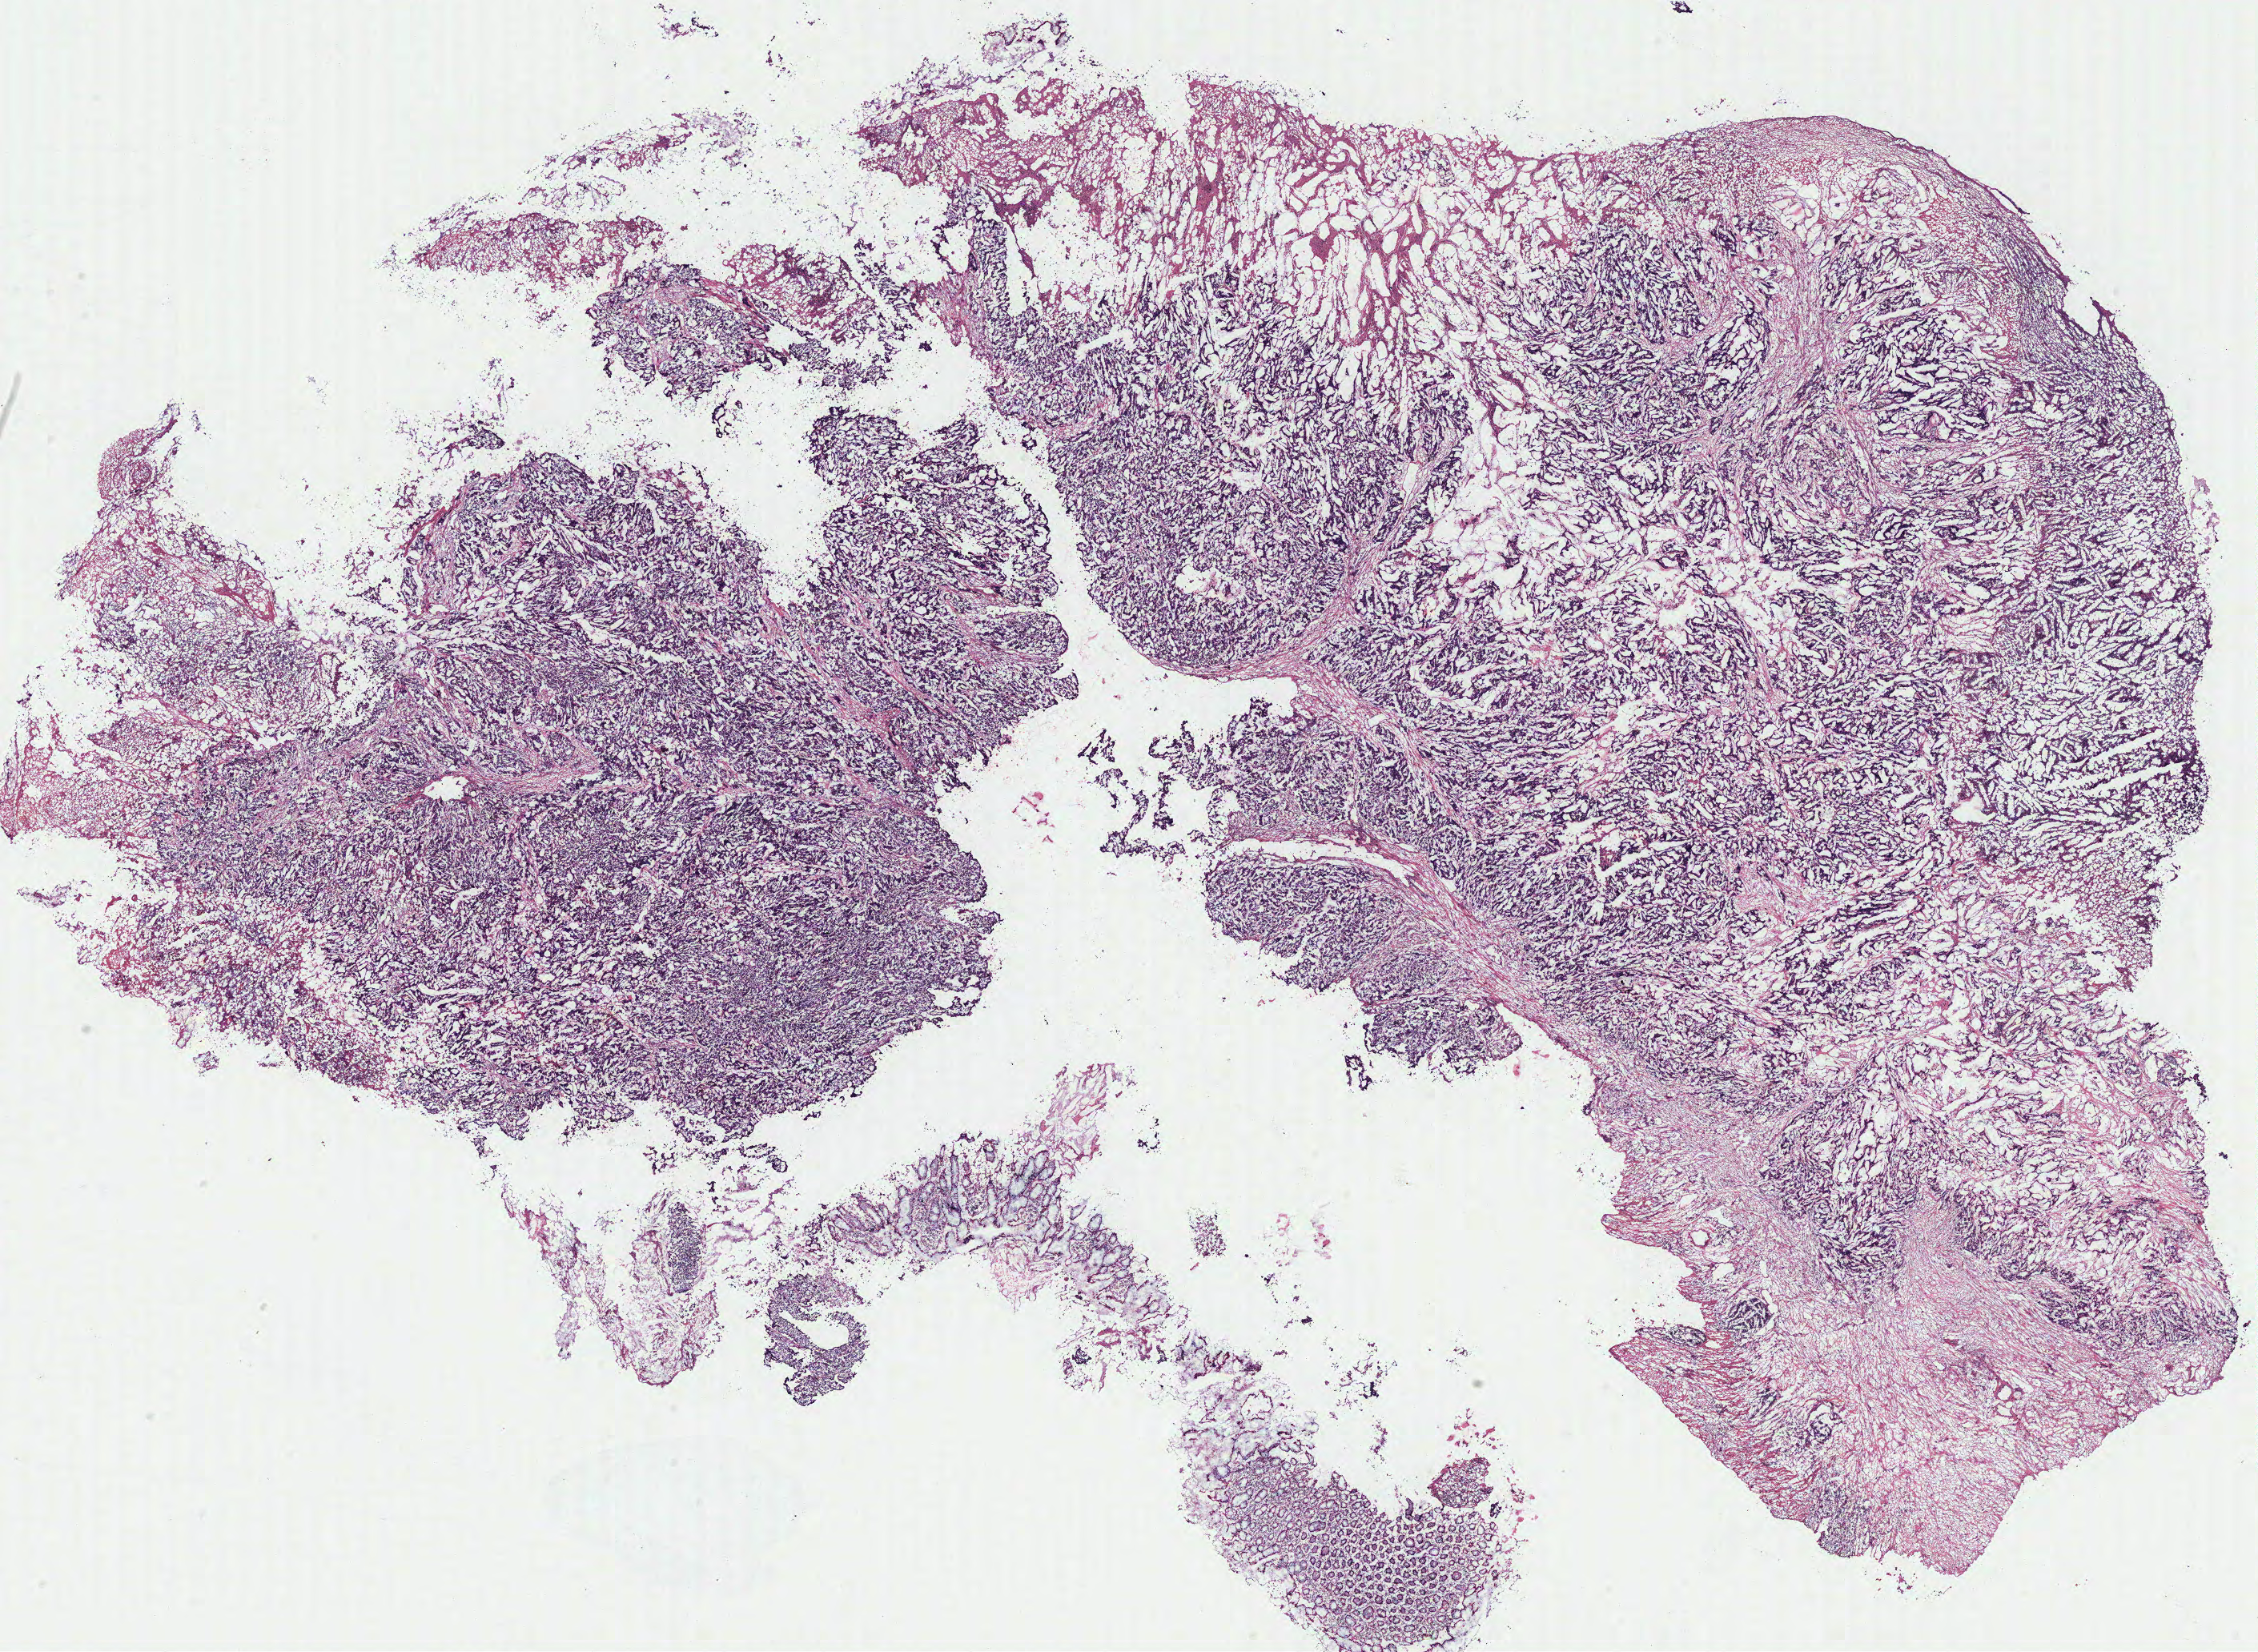
Digitized H&E tissue section (whole slide) — whole scanned area (about 22.6 x 16.5 mm) shown as a low-resolution overview, colon, tumour tissue. Female, 64 y/o.
Histologic diagnosis: Adenocarcinoma, NOS.